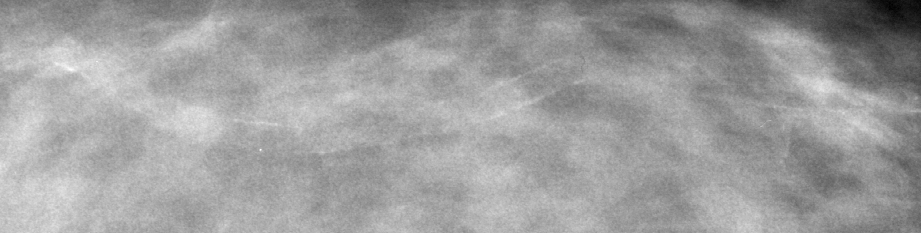
Region of interest cut from a scanned film mammogram (one marked finding); left breast; CC view; BI-RADS breast density category 2 (scale 1–4).
Finding: calcifications, morphology vascular; BI-RADS assessment category 2; benign without callback (not worked up further).